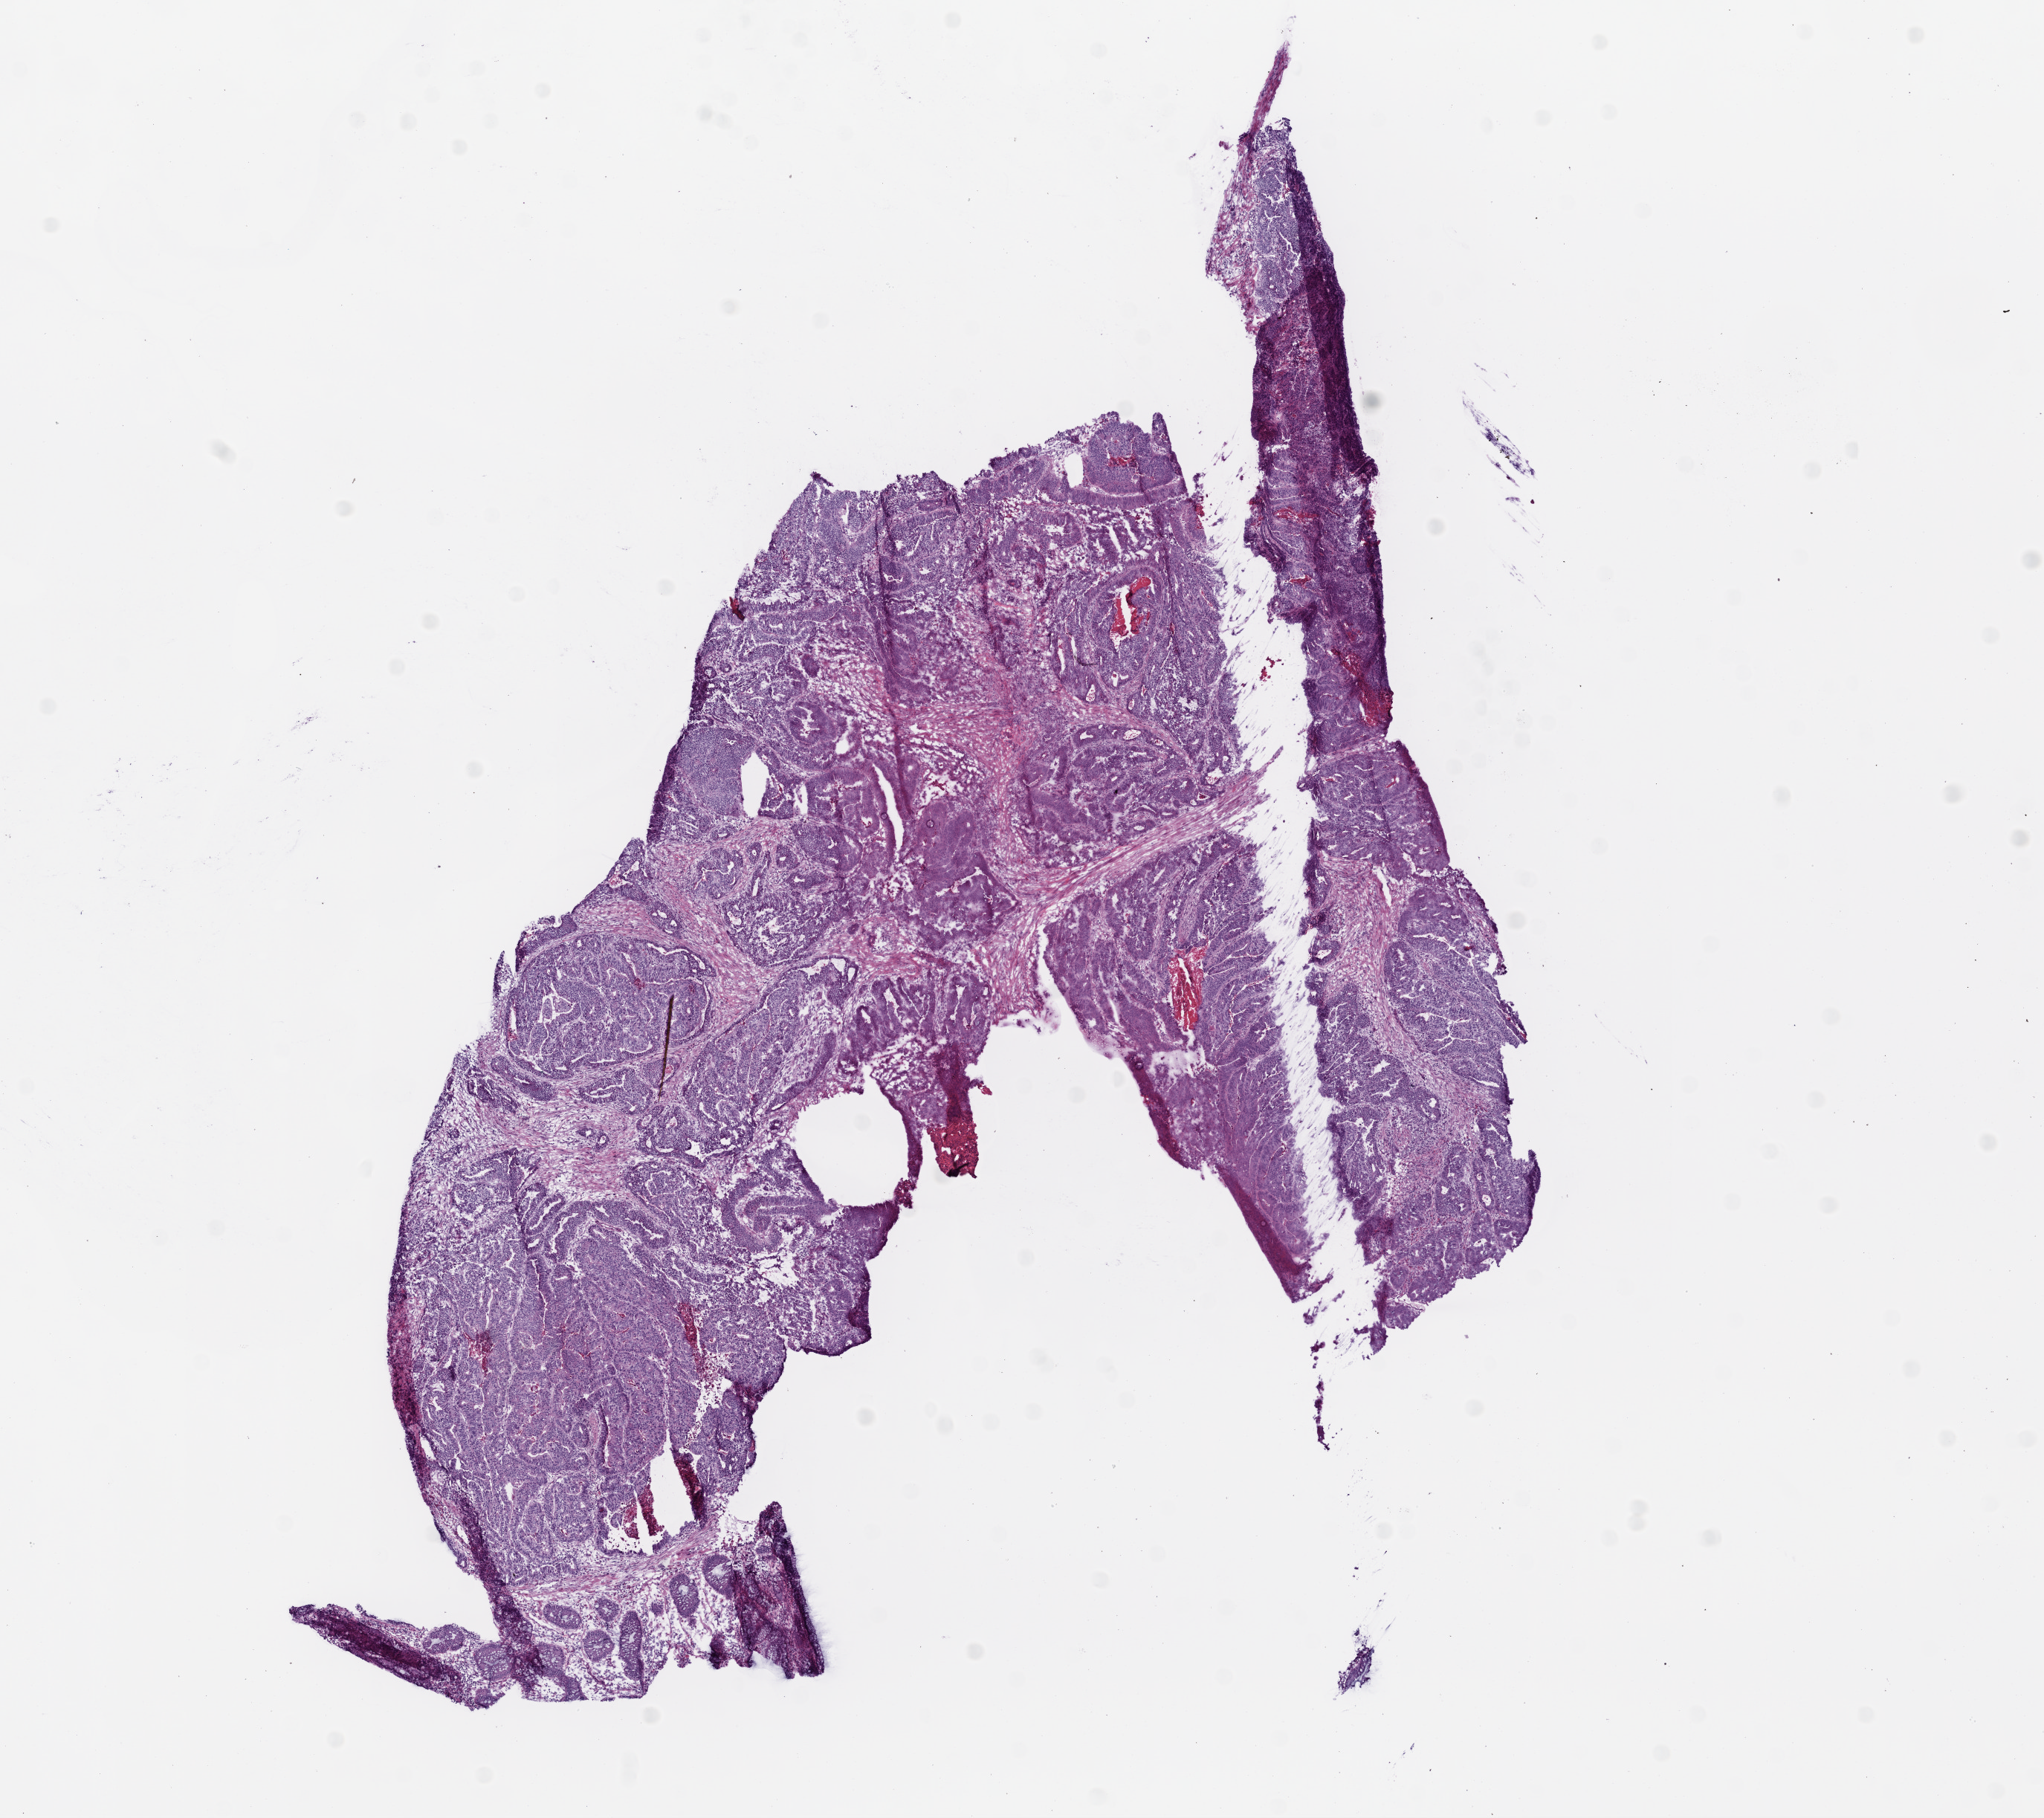
Digitized Hematoxylin and eosin (H&E) stained tissue section (whole slide), a low-resolution overview of the entire scanned area, about 11.0 x 9.8 mm (from a 20x scan). Frozen section from the top of the tissue portion. Primary tumour sample from the colon. Female, age 54 years at initial diagnosis. Slide review estimates, as recorded: tumour cells 80%, tumour nuclei 75%, normal cells 0%, stromal cells 12%, necrosis 8%.
* histologic diagnosis: Adenocarcinoma, NOS
* AJCC pathologic stage: II (5th edition)
* lymph nodes positive (case pathology): 0 of 27 examined